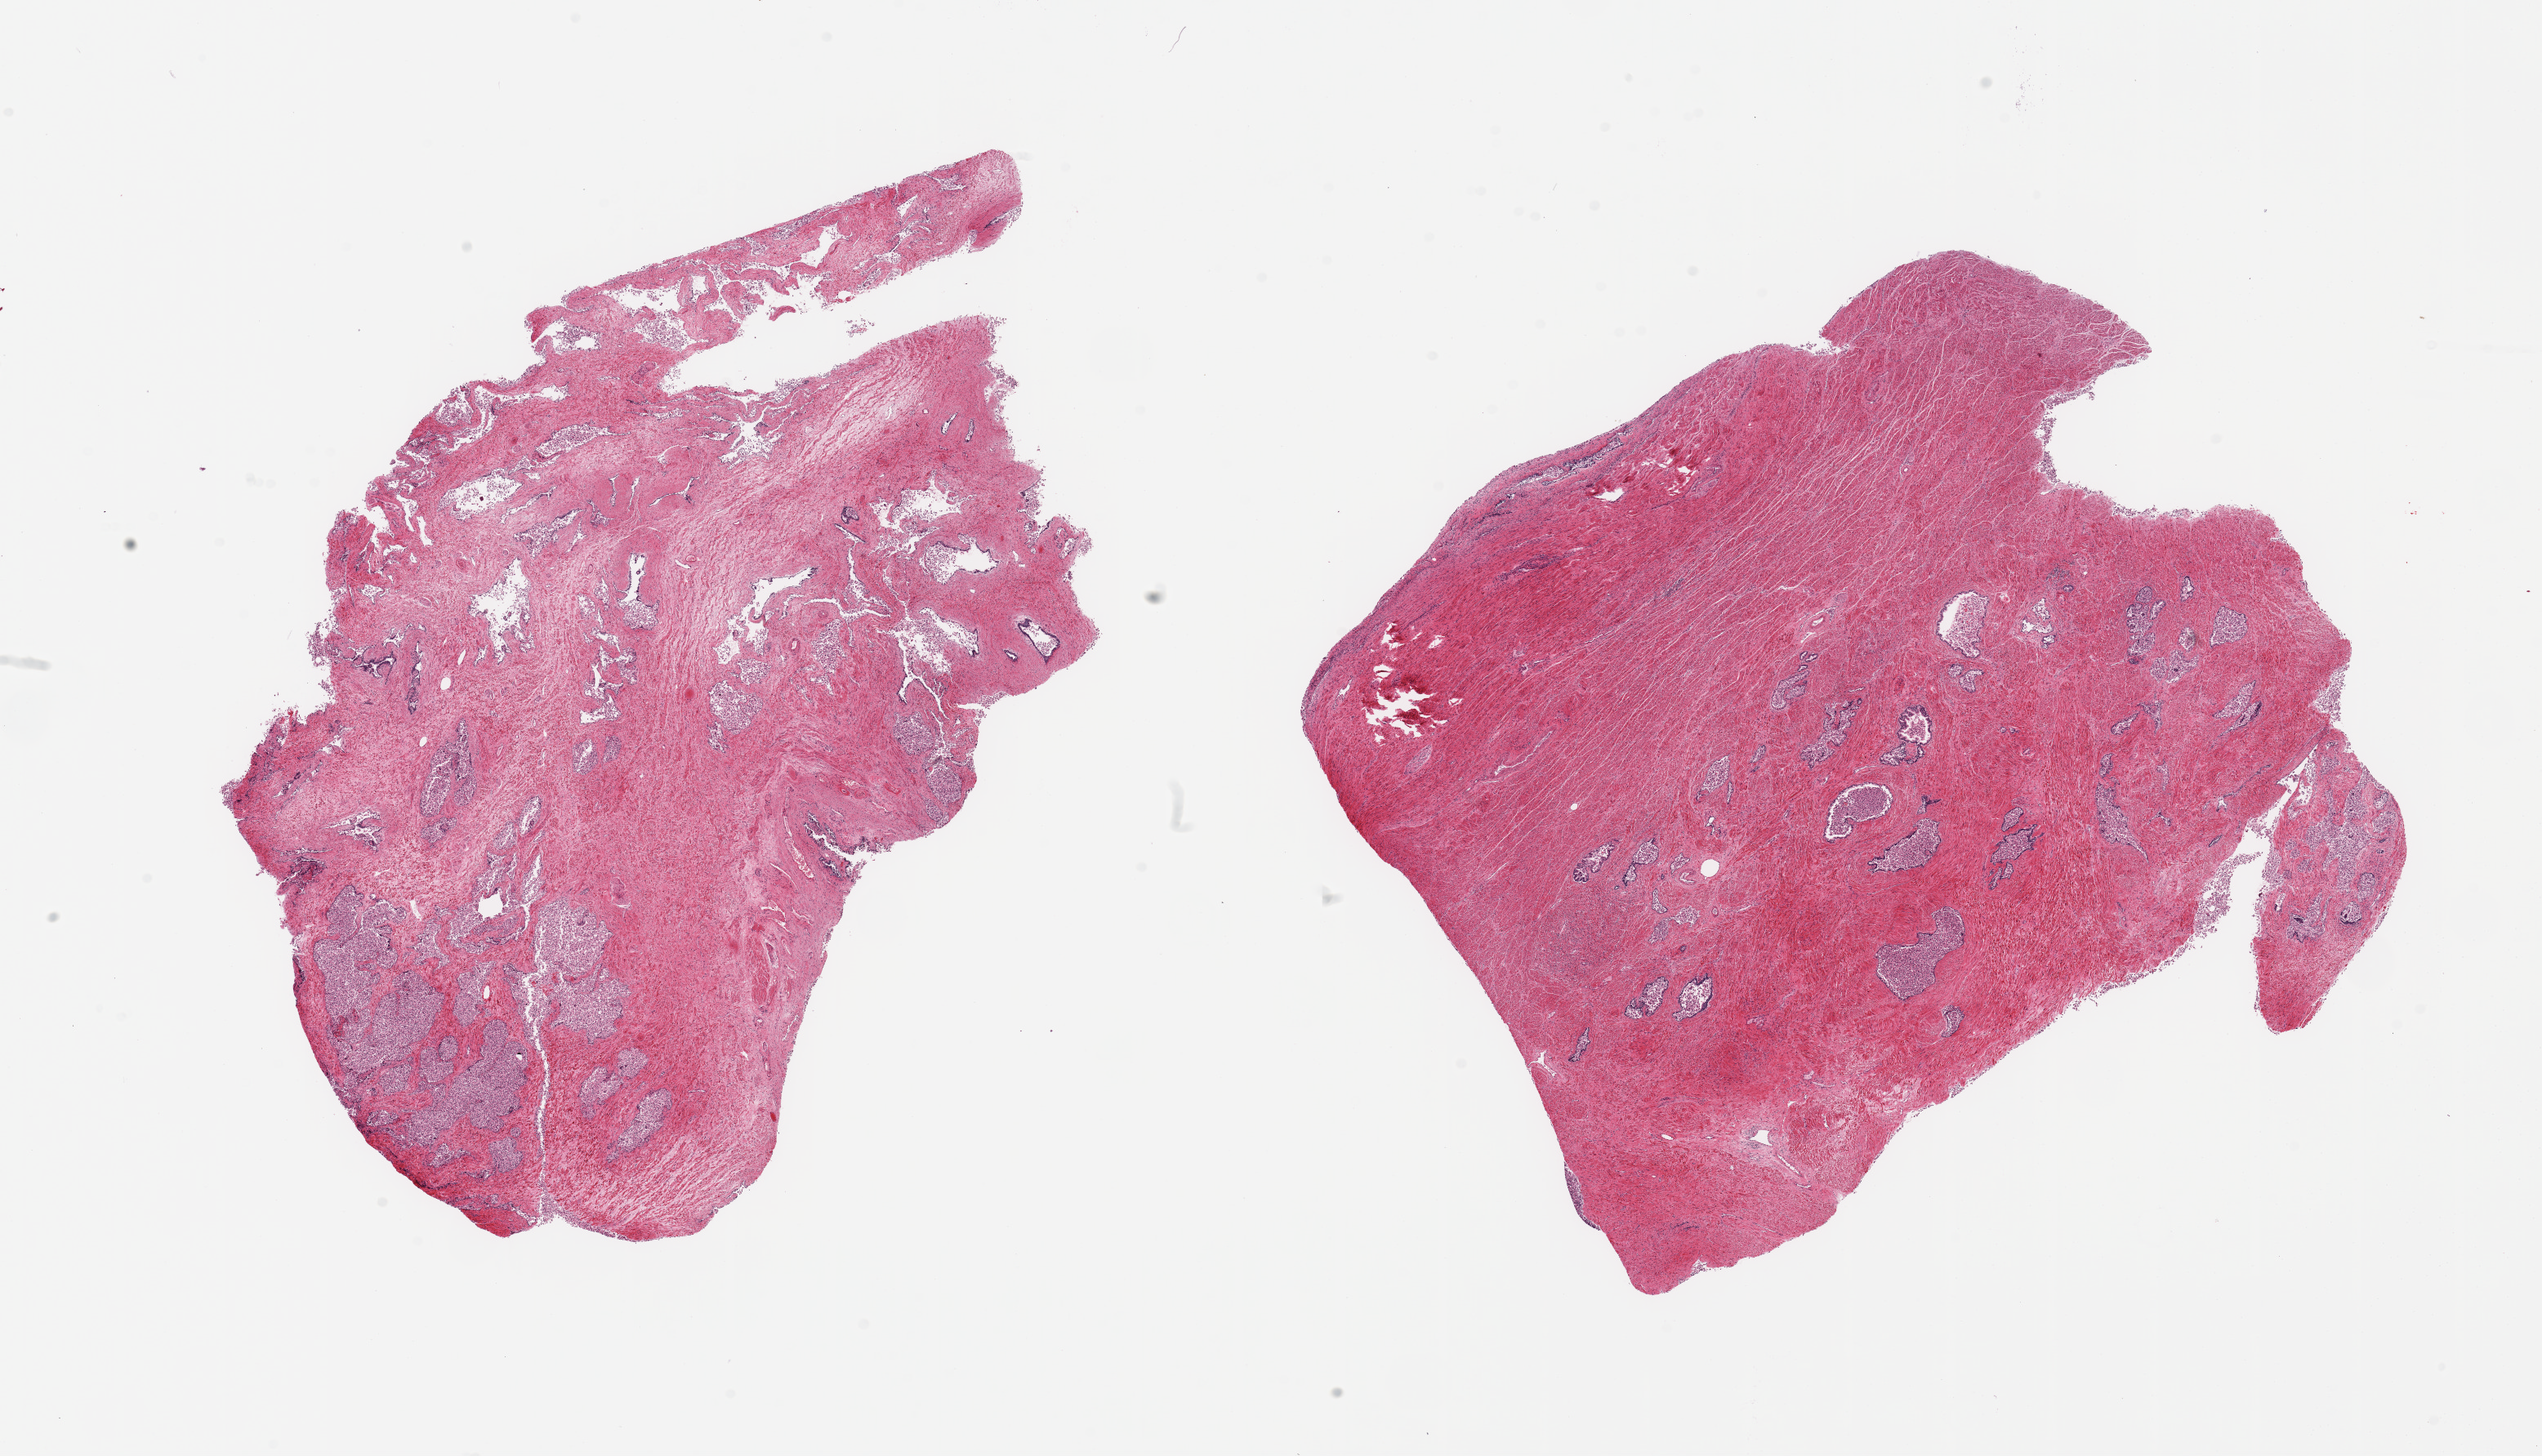
H&E whole-slide image, brightfield, shown as a low-resolution overview of the whole scanned area (about 24.6 x 14.1 mm). PAXgene-fixed paraffin-embedded (PFPE) section. Target tissue: prostate. Donor tissue sample. Donor: male.
* pathologist's review note for this sample: 2 pieces; glandular epithelium severely autolyzed, stroma intact